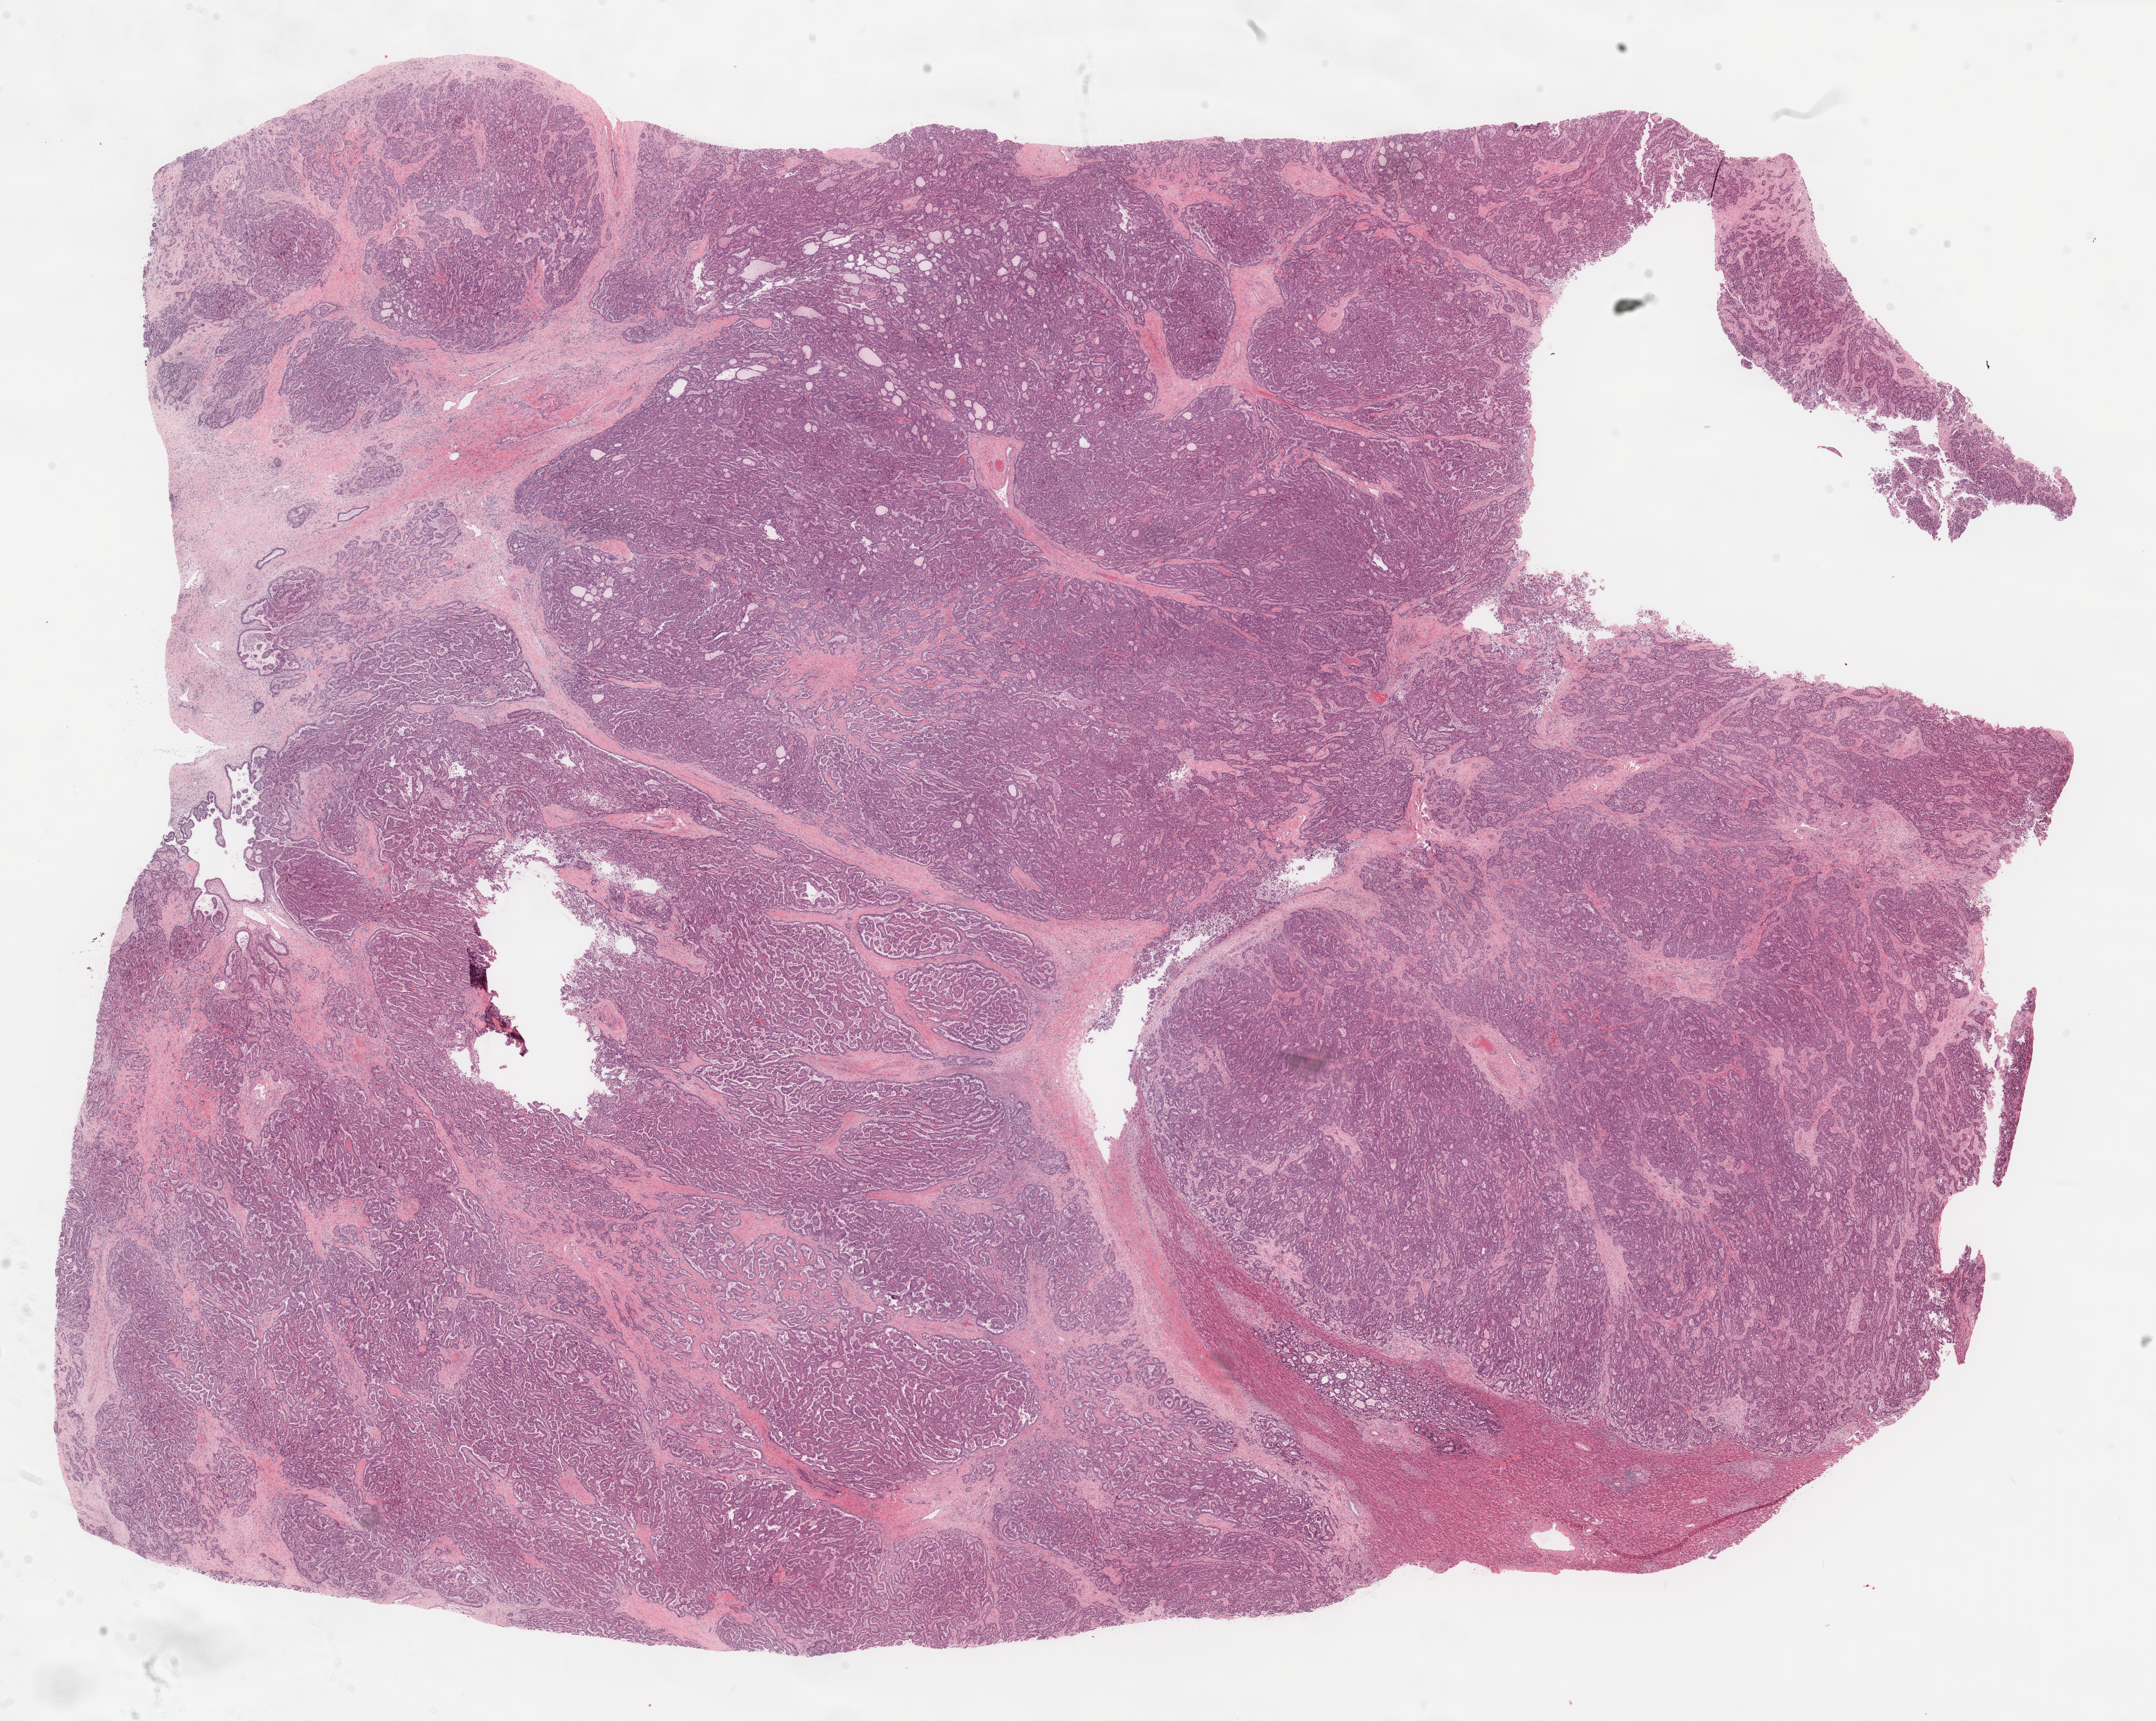
Digitized H&E-stained tissue section (whole slide) — low-resolution overview of the scanned area, about 24.2 x 19.4 mm. FFPE section. Bile duct, primary tumour sample. Female, age 59 years at initial diagnosis. Histologic grade: G2 (moderately differentiated).
TNM: T1 NX M0. Histologic diagnosis: Cholangiocarcinoma. AJCC pathologic stage: I (7th edition).